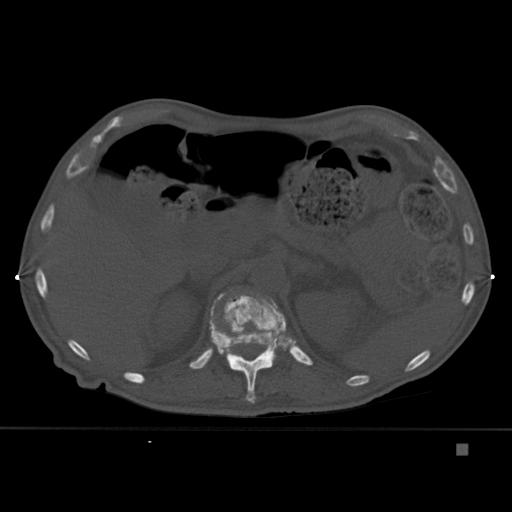
CT including the spine, one axial slice. Slice 197 of 451 in the series (ordered by position). Bone window (W 1800 / L 400 HU). 1.5 mm slice thickness. 512 × 512 image matrix, field of view 378 × 378 mm. Patient: male, 75 years. Case-level facts recorded for this patient, not image findings: primary cancer: prostate.
Annotated regions visible in this slice (semi-automatic segmentation, software-assisted and operator-edited):
- T12 vertebra: bounding box (x1, y1, x2, y2) in pixels: (208, 289, 286, 403)